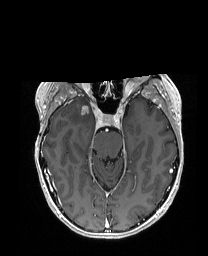
Brain MRI from a brain-tumour surgery series, one axial slice; position 116 of 192 along the scan axis; T1-weighted post-contrast; 1 mm slice thickness; 208 × 256 image matrix, field of view 203 × 250 mm. Case-level facts recorded for this patient, not image findings: histopathology: Metastatic Carcinoma from Breast primary; tumour location: Right Frontal.
Annotated regions visible in this slice (outlined manually by an expert reader):
- tumour: bounding box (x1, y1, x2, y2) in pixels: (96, 104, 102, 112)